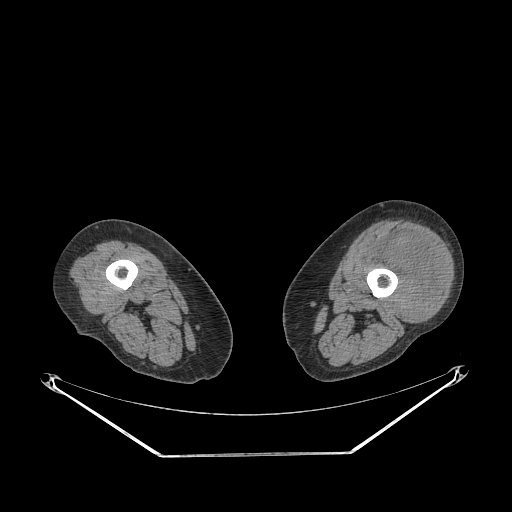
CT of an extremity soft-tissue mass (from a PET/CT study), one axial slice. Position 209 of 267 along the scan axis. Reconstruction kernel STANDARD. Soft-tissue window (W 400 / L 40 HU). 3.75 mm slice thickness. 512 × 512 image matrix, field of view 500 × 500 mm. Female patient. Case-level facts recorded for this patient, not image findings: histological type: undifferentiated – high grade; grade: high; site of the primary tumour: left thigh.
Outlined on this slice (expert contour drawn on MRI and transferred to this co-registered scan by the dataset authors):
- gross tumour volume including surrounding oedema: bounding box (x1, y1, x2, y2) in pixels: (367, 231, 446, 318)
- gross tumour volume (mass): (381, 231, 444, 318)